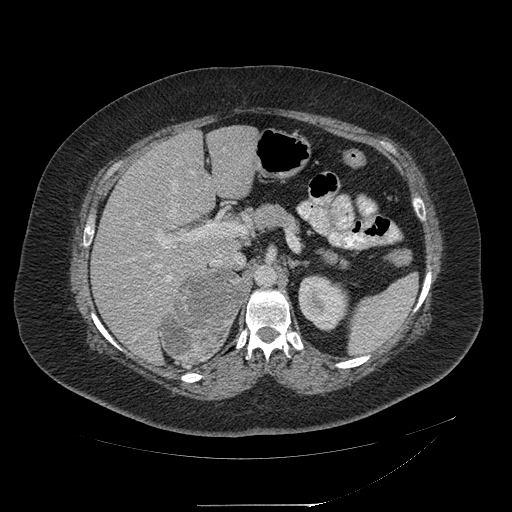
Contrast-enhanced abdominal CT, one axial slice. Position 133 of 217 along the scan axis. Reconstruction kernel STANDARD. 120 kVp. Intravenous contrast given. Soft-tissue window (W 400 / L 40 HU). 1.25 mm slice thickness. 512 × 512 image matrix, field of view 453 × 453 mm. Patient: female, 55 years. Case-level facts recorded for this patient, not image findings: diagnosis: adrenocortical carcinoma; tumour side: right adrenal; tumour size at pathology: 11 cm; Ki-67 index: 20 %; stage (as recorded): 2.
Structures marked on this image (semi-automatic segmentation, software-assisted and operator-edited):
- mass: bounding box <161,272,245,364> (left, top, right, bottom; pixels)